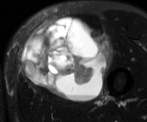
MRI of an extremity soft-tissue mass, one axial slice; position 28 of 52 along the scan axis; T2-weighted fat-saturated; MR volume resampled by the dataset authors to the PET/CT grid (not the native acquisition matrix); 3.27 mm slice thickness; 147 × 122 image matrix, field of view 144 × 119 mm. Male patient. From the clinical record (not read from this slice): histological type: pleiomorphic liposarcoma; grade: high; site of the primary tumour: left thigh.
Structures marked on this image (expert contour drawn on MRI and transferred to this co-registered scan by the dataset authors):
- gross tumour volume including surrounding oedema: bounding box [x1, y1, x2, y2] px = [21, 16, 115, 100]
- gross tumour volume (mass): [21, 16, 111, 100]